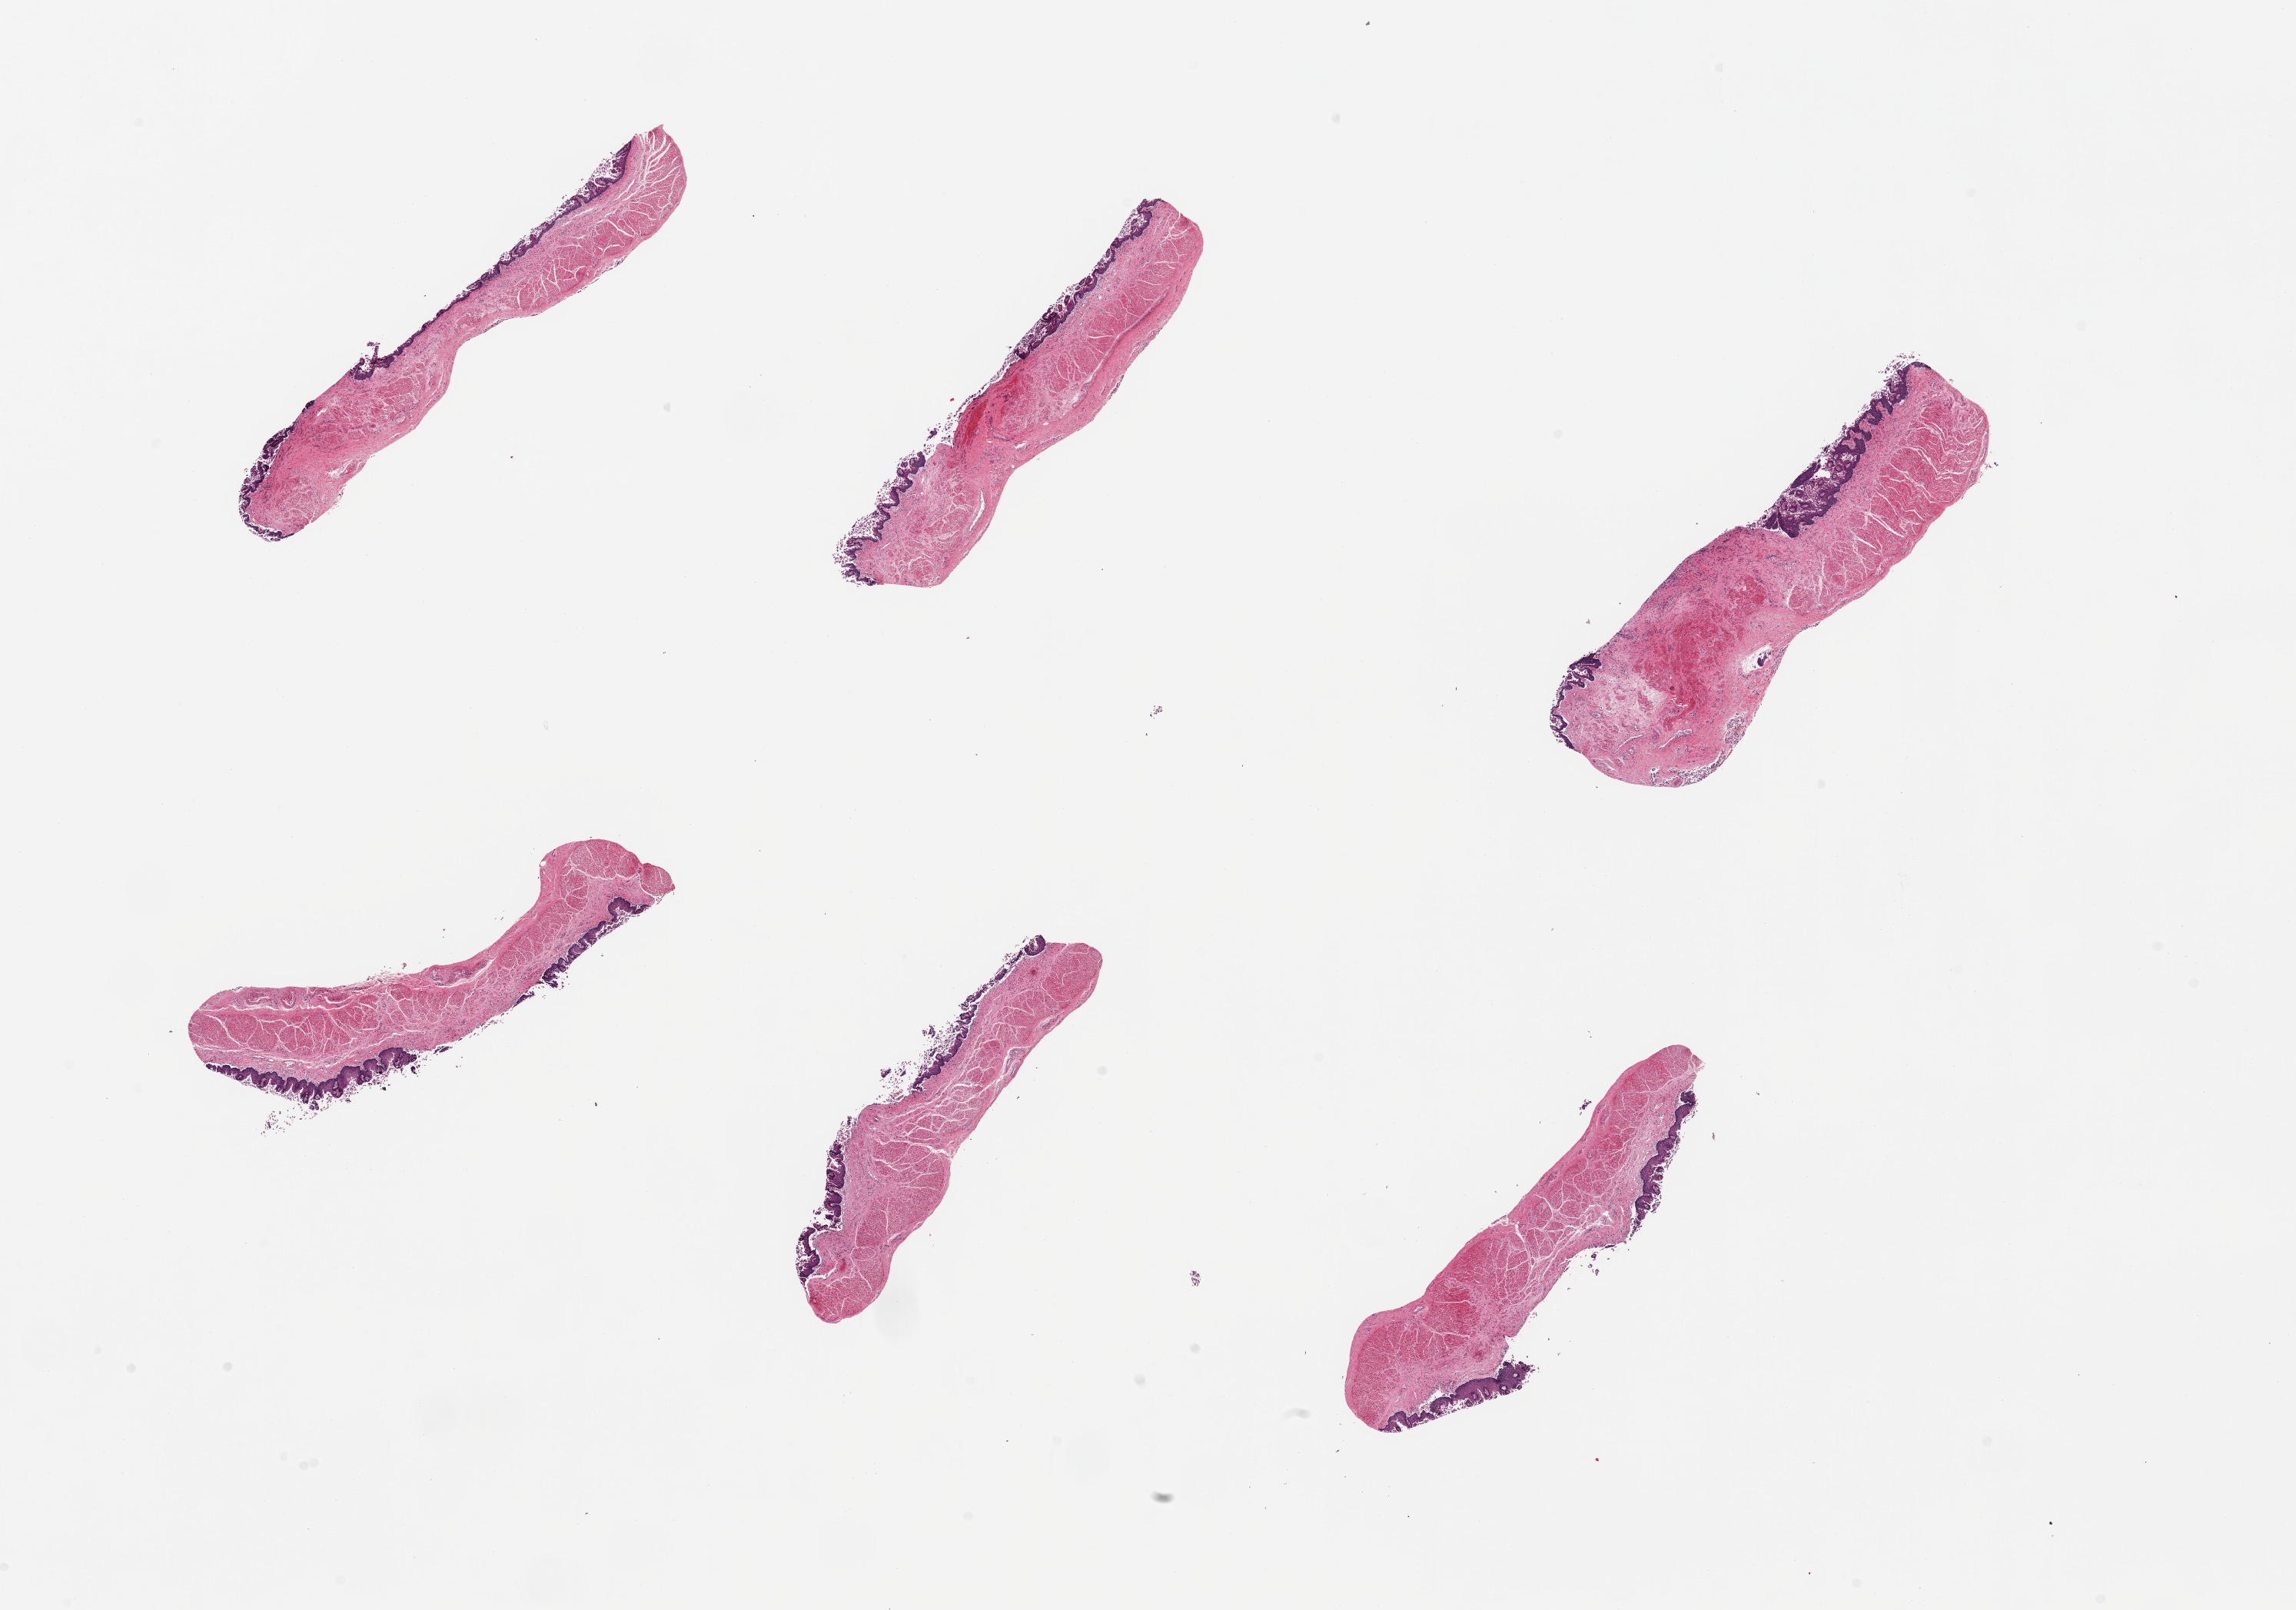
Whole-slide image, H&E stain — shown as a low-resolution overview of the whole scanned area (about 23.6 x 16.6 mm), PAXgene-fixed paraffin-embedded (PFPE) section, sampled site (target tissue): esophageal mucous membrane, tissue donor sample.
Reviewer comment on this tissue sample: 6 pieces, squamous mucosa sloughing.